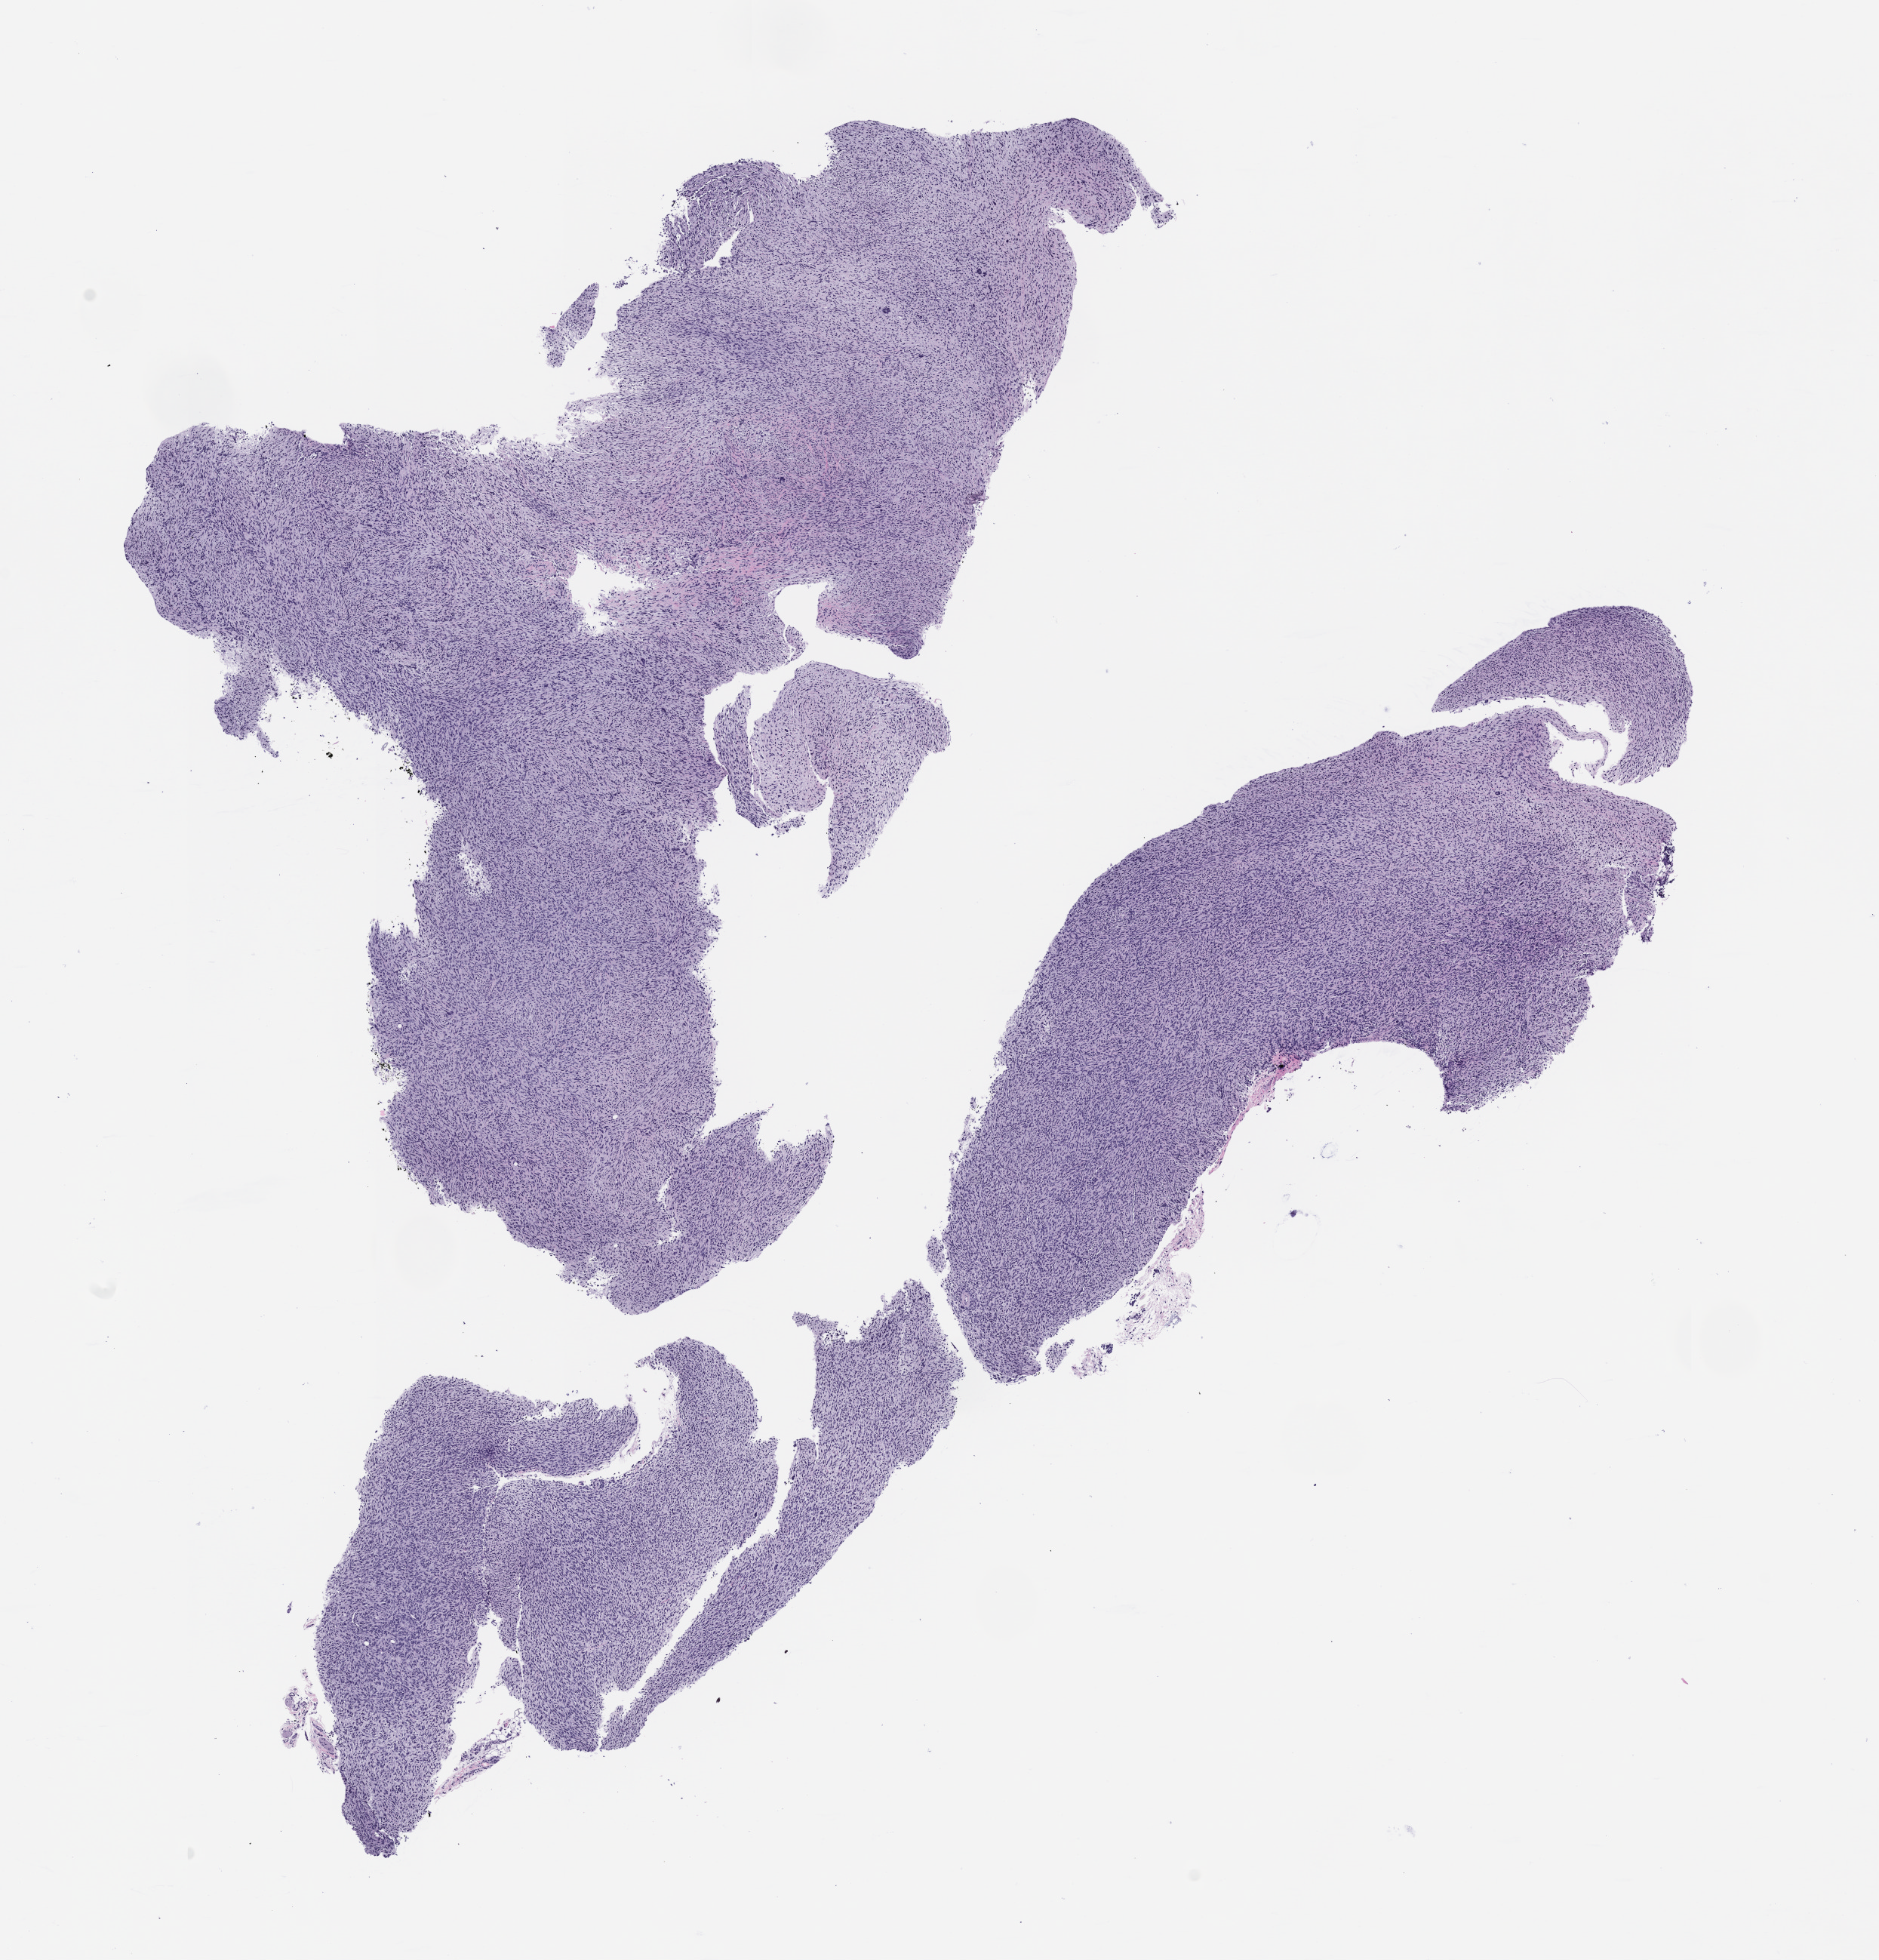
Hematoxylin and eosin (H&E) whole-slide image of a patient-derived xenograft (PDX) tumor grown in a mouse, passage 1, a low-resolution overview of the entire scanned area, about 10.0 x 10.4 mm; FFPE section; originating tumor site category: peripheral nervous system.
Originating patient diagnosis: Malignant Peripheral Nerve Sheath Tumor.